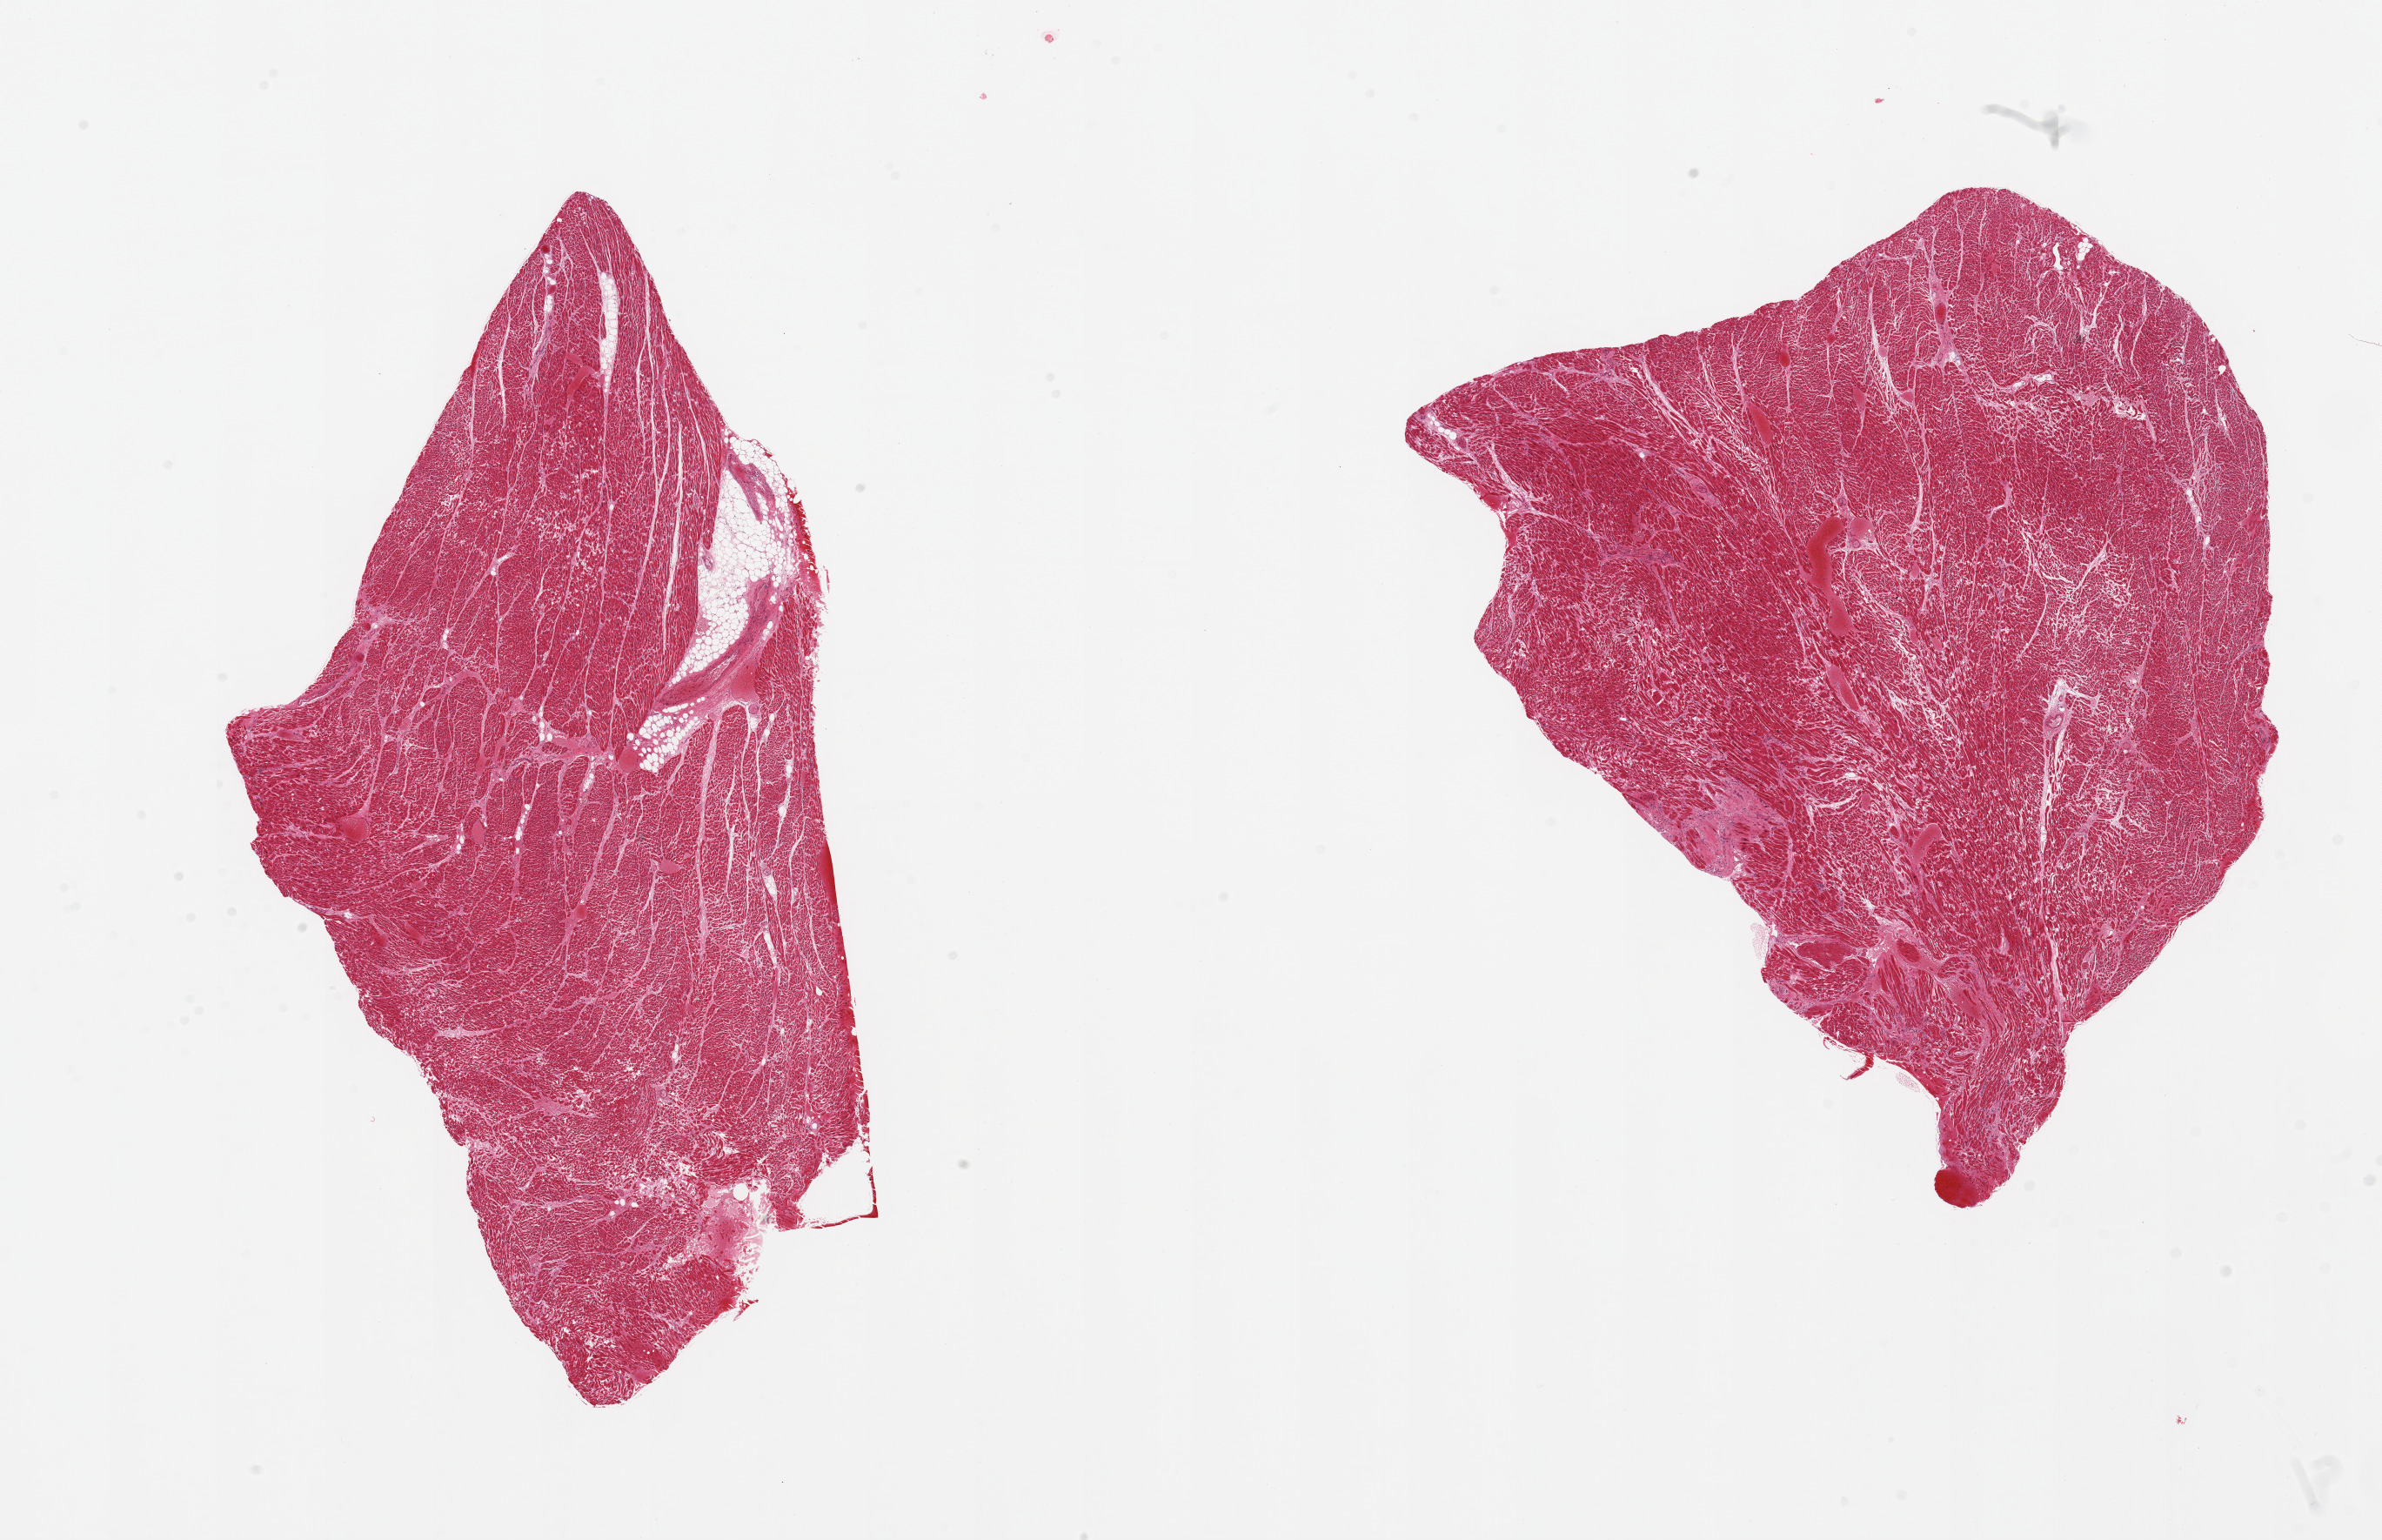
Whole-slide image, H&E stain, low-resolution overview of the scanned area, about 21.7 x 14.0 mm (from a 20x scan), PAXgene-fixed, paraffin-embedded tissue, section of heart (target tissue), tissue donor sample. Female donor.
Review note (as recorded): 2 pieces; bands of hypereosinophilic fibers suggest ischemia; focal scarring.